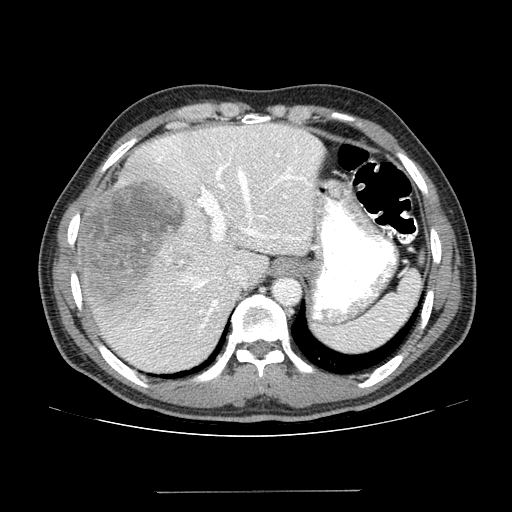
Contrast-enhanced abdominal CT (liver protocol), one axial slice. Slice 103 of 131 in the series (ordered by position). Reconstruction kernel STANDARD. 100 kVp. One of 2 acquisitions stored at this slice position. Soft-tissue window (W 400 / L 40 HU). 2.5 mm slice thickness. 512 × 512 image matrix. From the clinical record (not read from this slice): diagnosis: hepatocellular carcinoma (patient treated with transarterial chemoembolisation; whether this scan precedes or follows treatment is not stated here); TNM stage (as recorded): Stage-I; Child-Pugh class: A.
Outlined on this slice (semi-automatic segmentation, software-assisted and operator-edited):
- abdominal aorta: bounding box [x1, y1, x2, y2] px = [275, 279, 299, 303]
- liver parenchyma outside the tumour (the mass and vessels are separate outlines, so this box may not span the whole liver): [76, 124, 324, 370]
- mass: [78, 178, 184, 315]
- liver vessels: [121, 128, 319, 364]